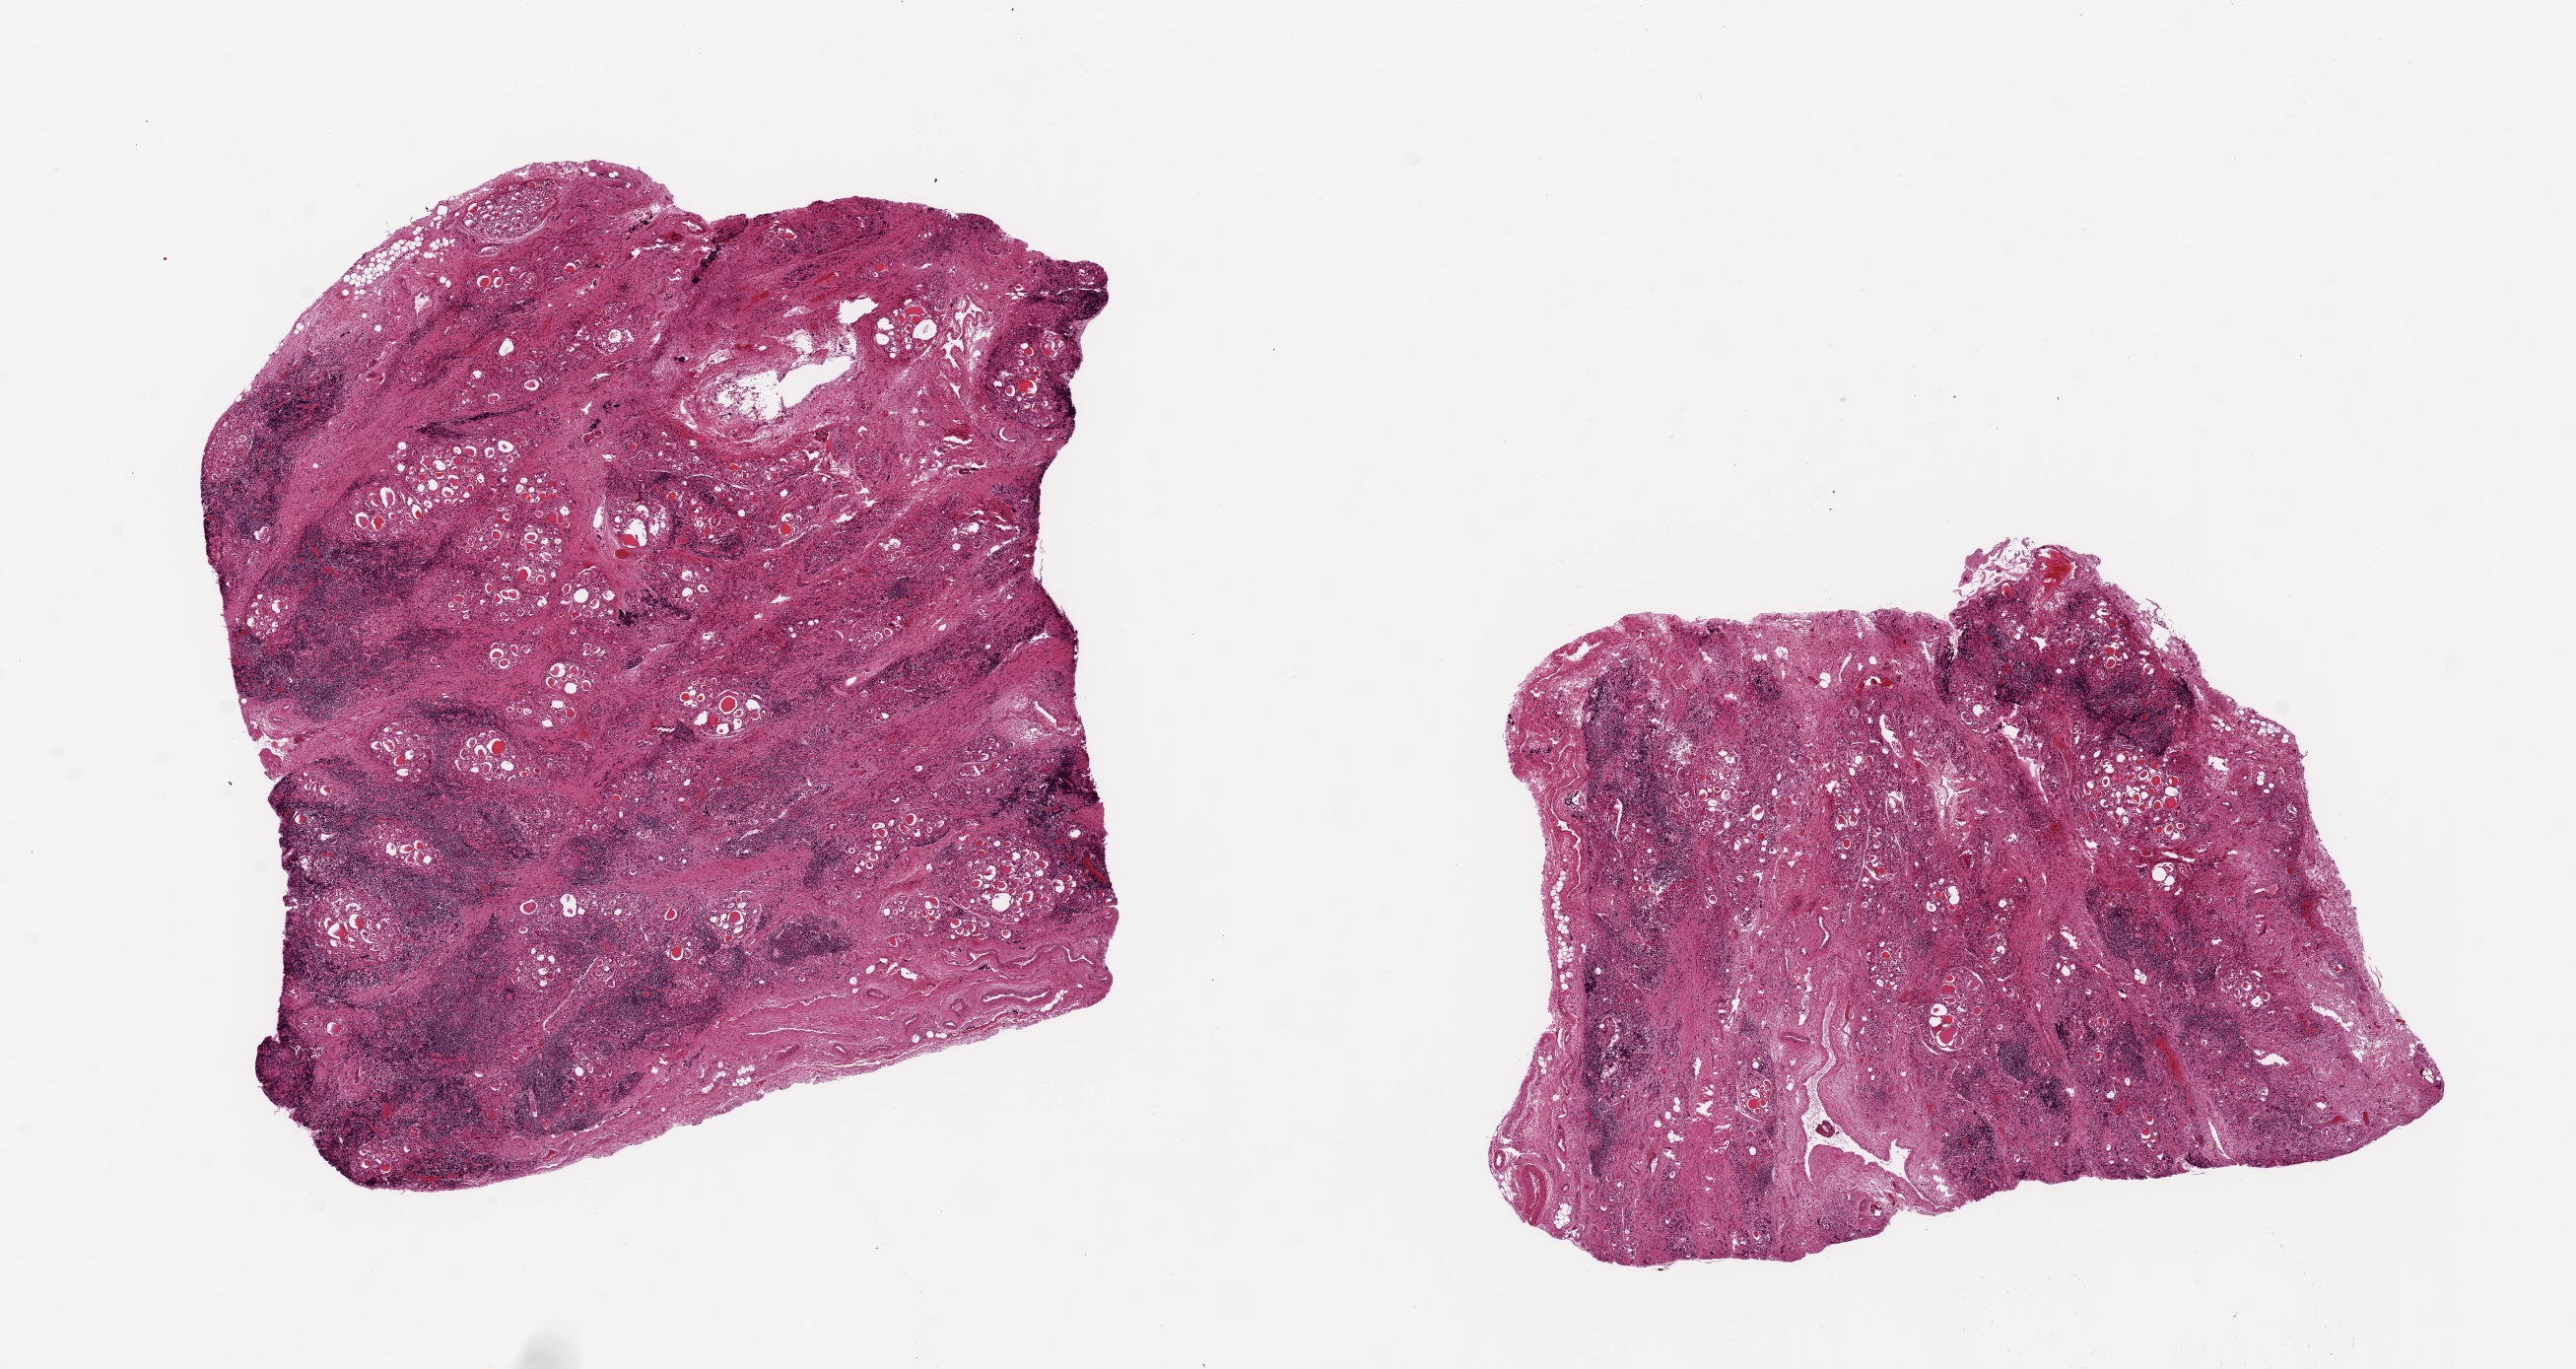
Digitized haematoxylin and eosin-stained section — a low-resolution overview of the entire scanned area, about 20.7 x 11.0 mm (acquisition: 20x scan). PAXgene-fixed, paraffin-embedded tissue. Target tissue: thyroid. Donor tissue sample. Donor sex: female.
Reviewer comment on this tissue sample: 2 pieces ~7x7mm. Prominent Hashimoto's thyroiditis, diffuse, in both, with regressive/involutional changes.